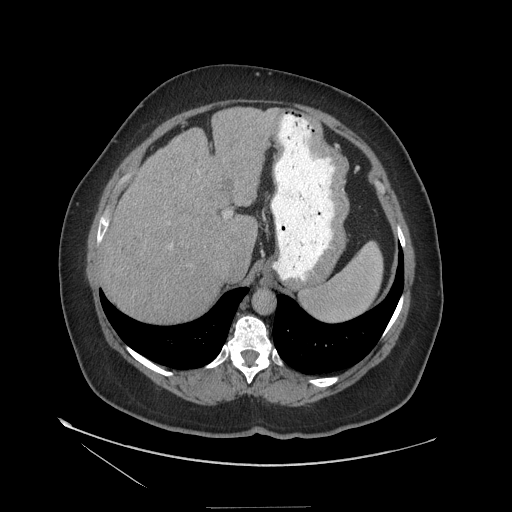
Contrast-enhanced abdominal CT (liver protocol), one axial slice. Position 87 of 127 along the scan axis. 140 kVp. Soft-tissue window (W 400 / L 40 HU). 2.5 mm slice thickness. 512 × 512 image matrix, field of view 480 × 480 mm. Case-level facts recorded for this patient, not image findings: diagnosis: hepatocellular carcinoma (patient treated with transarterial chemoembolisation; whether this scan precedes or follows treatment is not stated here); TNM stage (as recorded): Stage-II; Child-Pugh class: A.
Structures marked on this image (semi-automatically segmented with operator editing):
- abdominal aorta: bounding box [x1, y1, x2, y2] px = [254, 291, 275, 314]
- liver parenchyma outside the tumour (the mass and vessels are separate outlines, so this box may not span the whole liver): [98, 108, 280, 322]
- mass: [119, 230, 147, 259]
- liver vessels: [171, 171, 230, 246]